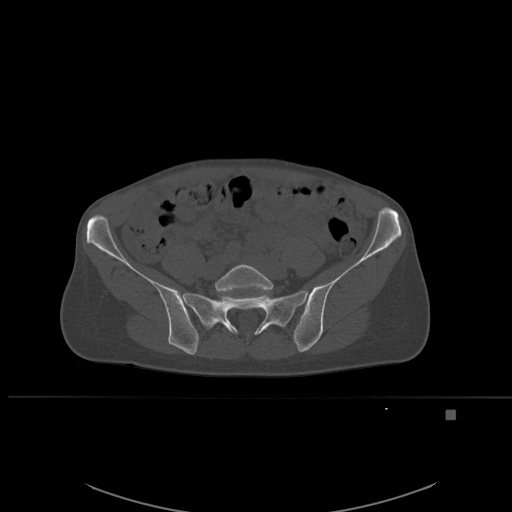
CT including the spine, one axial slice; position 162 of 537 along the scan axis; bone window (W 1800 / L 400 HU); 1.5 mm slice thickness; 512 × 512 image matrix, field of view 440 × 440 mm. Female patient, age 45 years. Case-level facts recorded for this patient, not image findings: primary cancer: lung.
Structures marked on this image (semi-automatically segmented with operator editing):
- L5 vertebra: bounding box <215,264,273,297> (left, top, right, bottom; pixels)